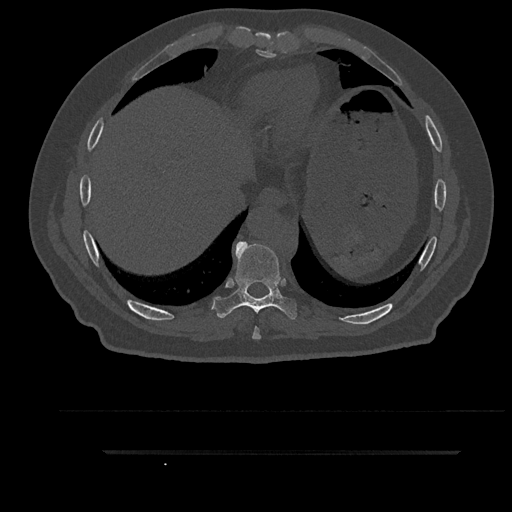
CT including the spine, one axial slice. Slice 430 of 797 in the series (ordered by position). Reconstruction kernel Br40s/3. 120 kVp. Bone window (W 1800 / L 400 HU). 0.5 mm slice thickness. 512 × 512 image matrix, field of view 432 × 432 mm. Male patient, age 63 years. Case-level facts recorded for this patient, not image findings: primary cancer: renal; vertebrae with lytic lesions (as recorded): T8.
Outlined on this slice (semi-automatic segmentation, software-assisted and operator-edited):
- T8 vertebra: bounding box <252,326,261,339> (left, top, right, bottom; pixels)
- T9 vertebra: <212,241,297,319>